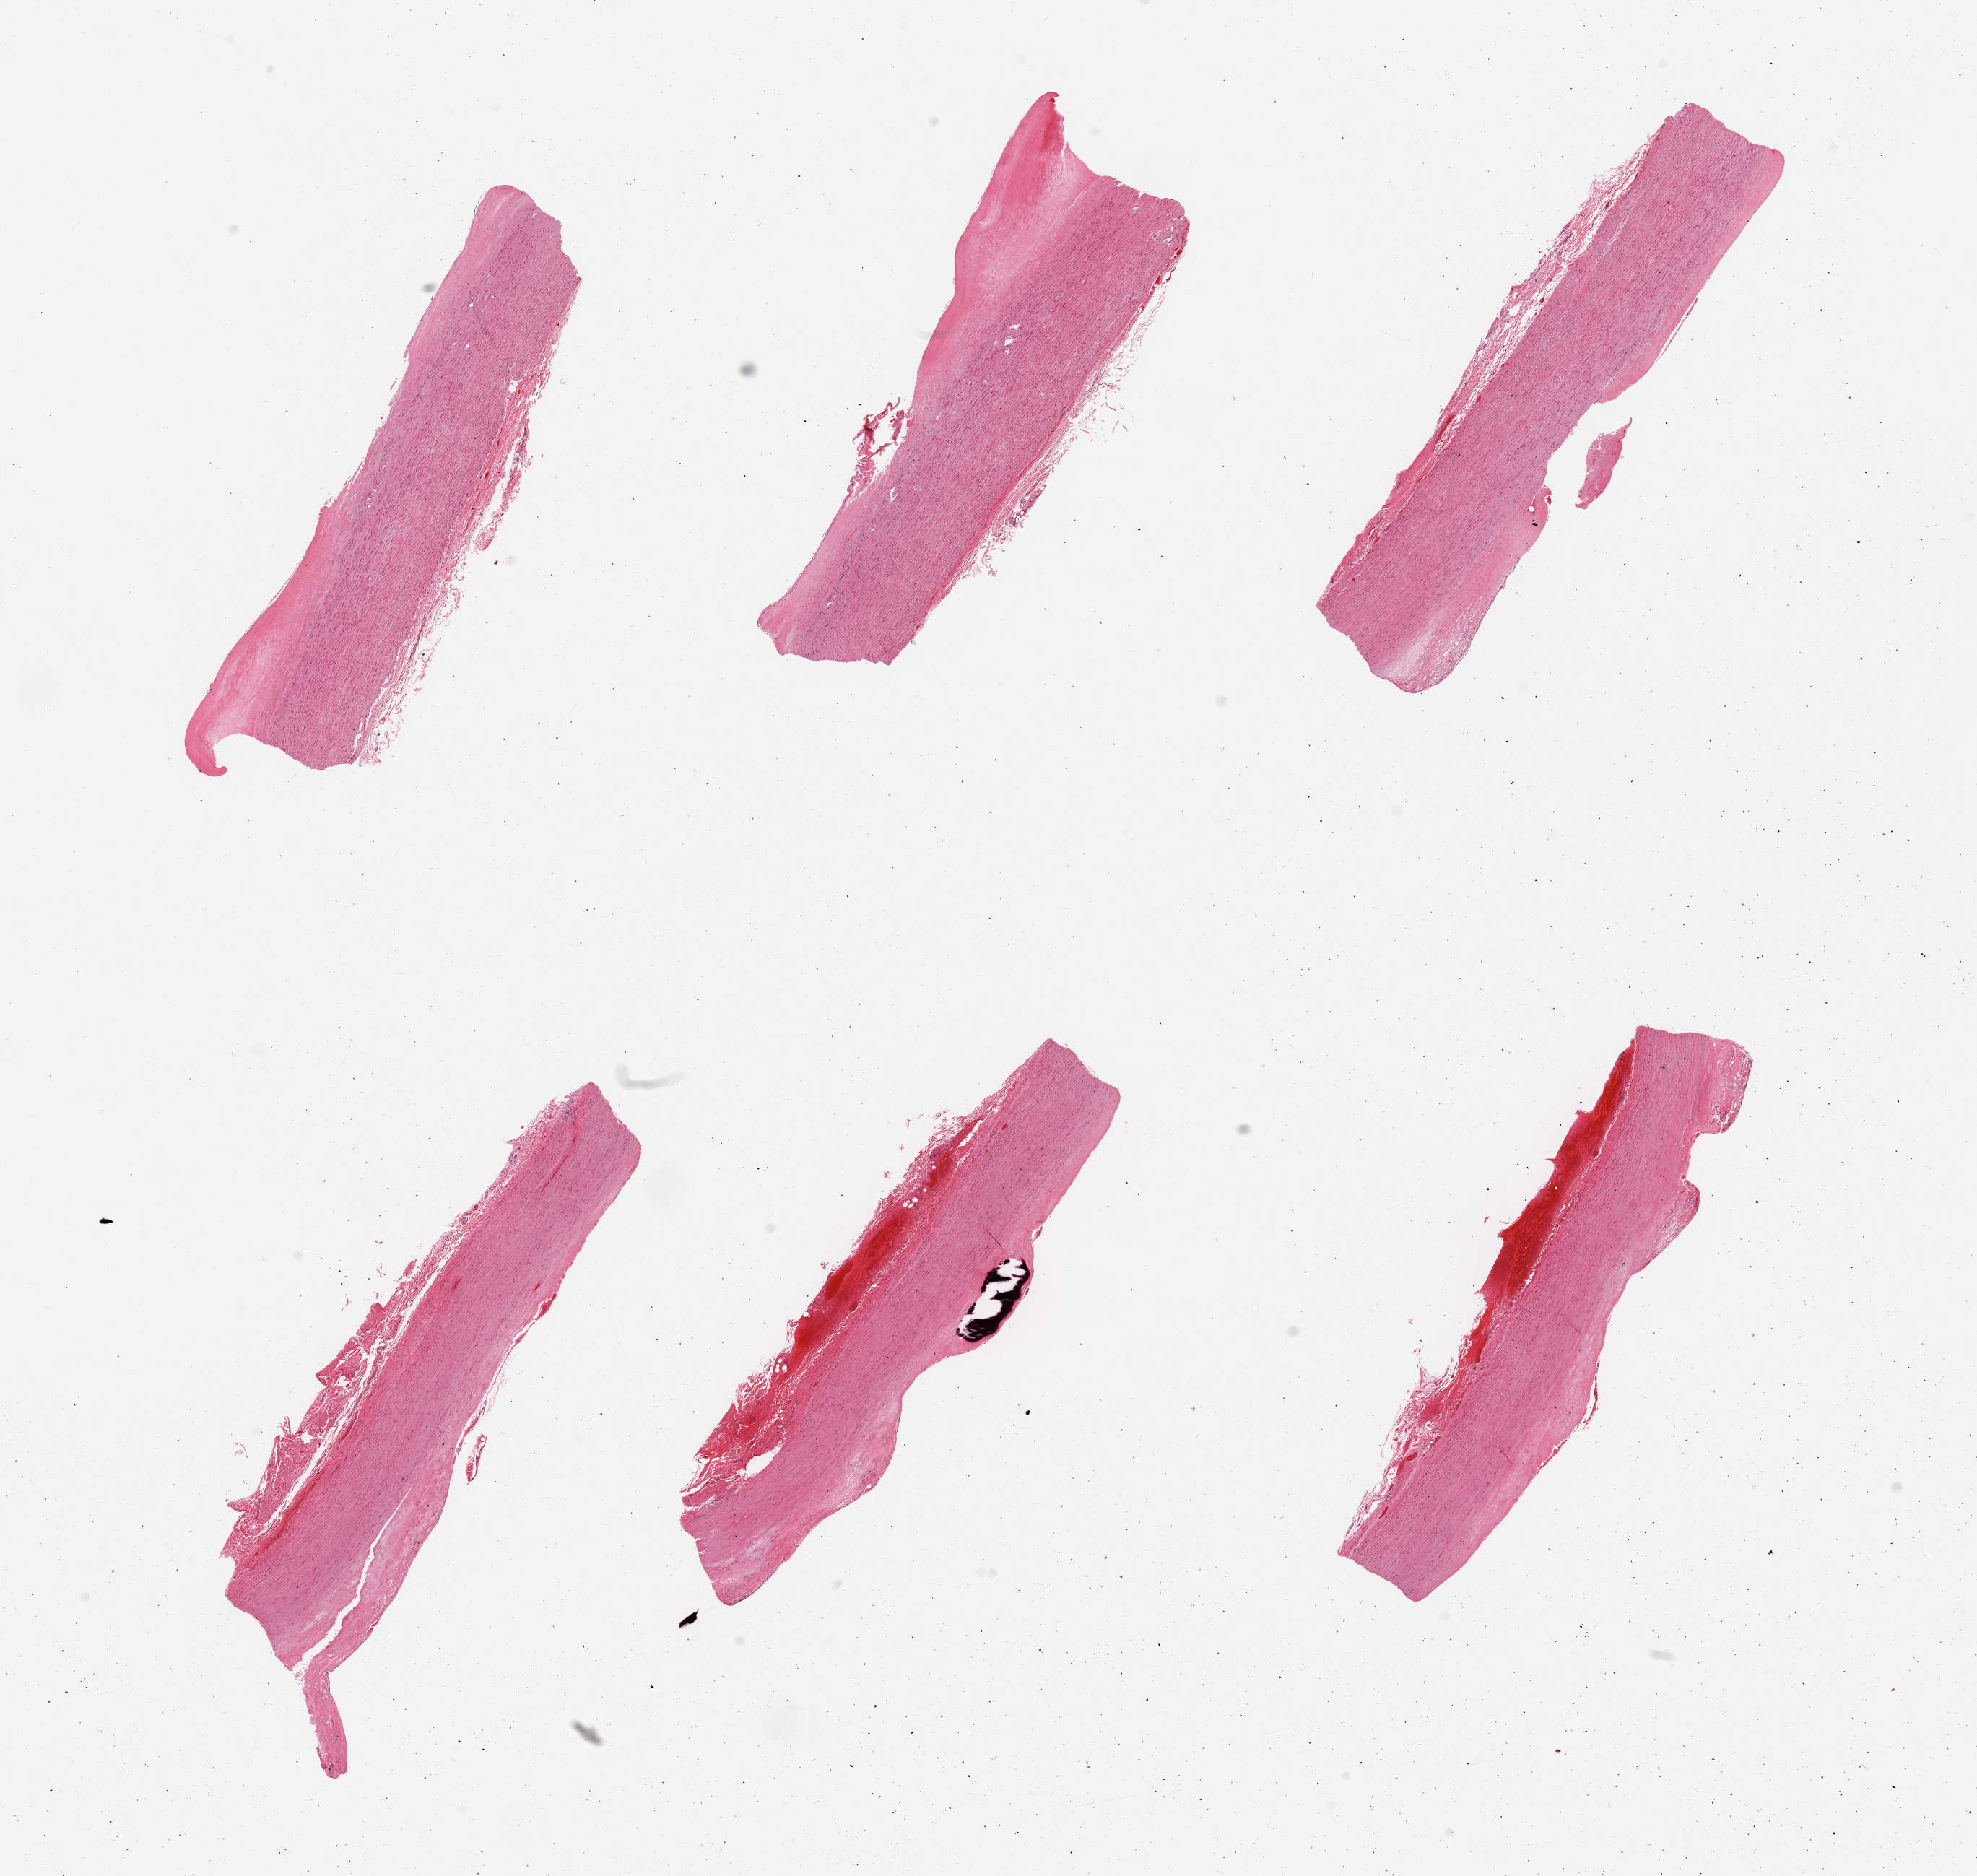
Whole-slide image, H&E stain — whole scanned area (about 21.7 x 20.5 mm, from a 20x scan) shown as a low-resolution overview. PAXgene-fixed, paraffin-embedded tissue. Target tissue: aorta. Donor tissue sample. Donor sex: female.
Reviewer comment on this tissue sample: 6 pieces; periaortic hemorrhage on 2 pieces; focal calcification in 1 plaque; flat plaques up to 0.7mm.